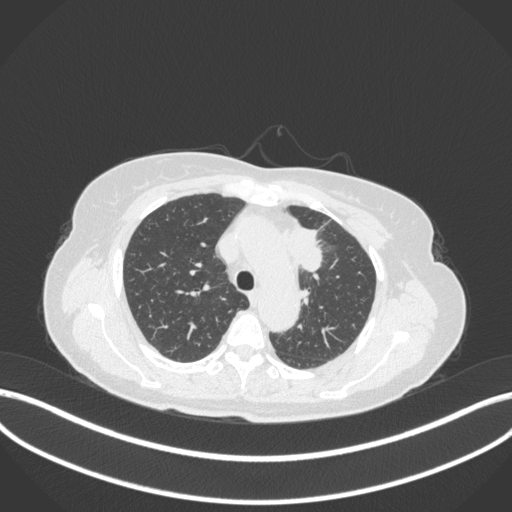
Chest CT, one axial slice. Position 244 of 368 along the scan axis. Lung window (W 1500 / L -600 HU). 512 × 512 image matrix, field of view 400 × 400 mm. Female patient, age 65 years. Case-level facts recorded for this patient, not image findings: clinical TNM (as recorded): T2a N0 M0; histopathological grade: G2-3.
Annotated regions visible in this slice (bounding box drawn by a radiologist):
- lung tumour (recorded histology: adenocarcinoma): bounding box <285,224,327,274> (left, top, right, bottom; pixels)